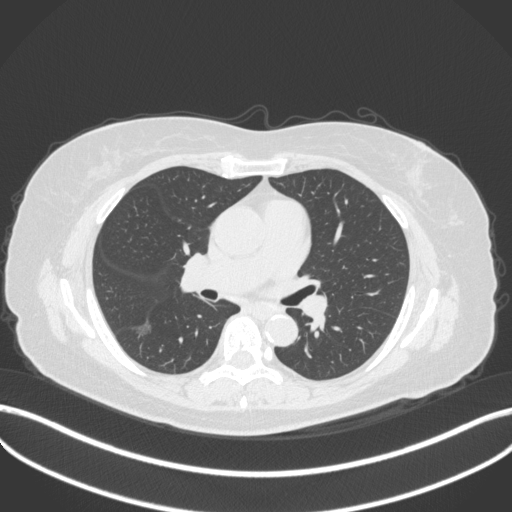
Chest CT, one axial slice; slice 179 of 322 in the series (ordered by position); reconstruction kernel B31f; 120 kVp; lung window (W 1500 / L -600 HU); 512 × 512 image matrix, field of view 400 × 400 mm. Patient: female, 64 years. Case-level facts recorded for this patient, not image findings: clinical TNM (as recorded): T1c N0 M0; histopathological grade: G1.
Annotated regions visible in this slice (bounding box drawn by a radiologist):
- lung tumour (recorded histology: adenocarcinoma): bounding box [x1, y1, x2, y2] px = [135, 315, 155, 339]